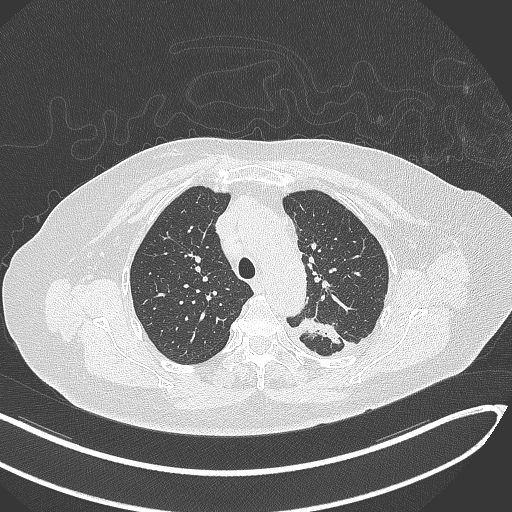
Chest CT, one axial slice. Reconstruction kernel B70f. Lung window (W 1500 / L -600 HU). 1 mm slice thickness. 512 × 512 image matrix, field of view 400 × 400 mm. Female patient, age 76 years. From the clinical record (not read from this slice): clinical TNM (as recorded): T1c N0 M0.
Outlined on this slice (bounding box drawn by a radiologist):
- lung tumour (recorded histology: adenocarcinoma): box from (x=291, y=315) to (x=347, y=350) px